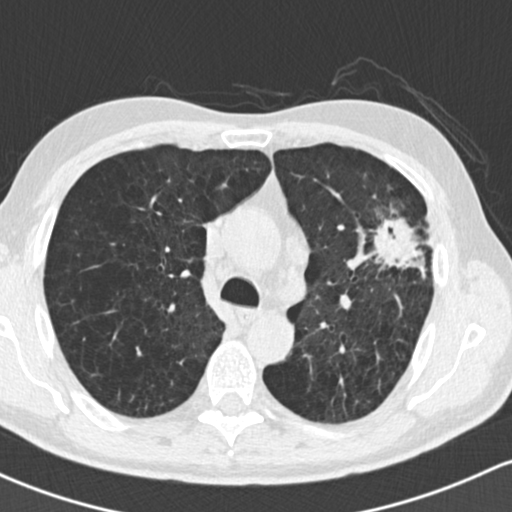
Low-dose screening chest CT, one axial slice. Position 106 of 162 along the scan axis. Reconstruction kernel B30f. 120 kVp. Lung window (W 1500 / L -600 HU). 512 × 512 image matrix.
Structures marked on this image (manually delineated by an expert):
- lesion 1 (tumor, upper lobe of left lung): bounding box [x1, y1, x2, y2] px = [371, 217, 425, 273]